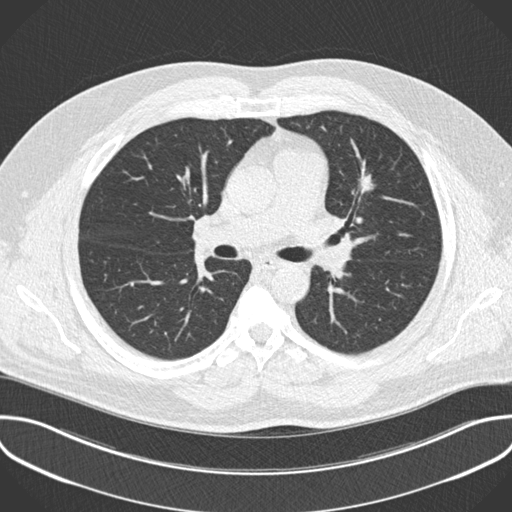
Axial slice from a low-dose chest CT screening exam, baseline annual screen, lung window (W 1500 / L -600 HU), 2 mm slice thickness, standard (soft-tissue) reconstruction kernel (B30f), 120 kVp. Male participant, aged 55 years at enrolment.
• Expert-annotated lung lesion, bounding box <346,159,390,194> (left, top, right, bottom; pixels).
• Screening reader's record for this exam (one nodule recorded; not confirmed to be the boxed lesion): non-calcified nodule or mass ≥4 mm, lingula, 13 × 12 mm, spiculated (stellate) margins, soft tissue attenuation.
• Participant outcome: lung cancer diagnosed 169 days after this screen — adenocarcinoma, NOS, left upper lobe, stage IA (AJCC 6th edition), 13 mm at pathology.